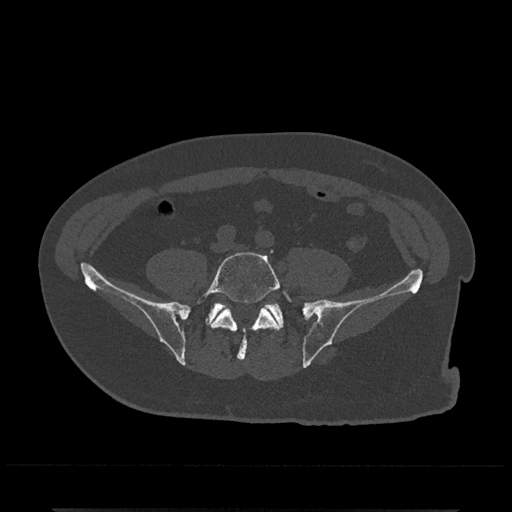
CT including the spine, one axial slice. Position 75 of 797 along the scan axis. Reconstruction kernel Br40s/3. Bone window (W 1800 / L 400 HU). 512 × 512 image matrix. Patient: male, 67 years. From the clinical record (not read from this slice): primary cancer: prostate.
Structures marked on this image (semi-automatic segmentation, software-assisted and operator-edited):
- L5 vertebra: bounding box <197,250,292,361> (left, top, right, bottom; pixels)